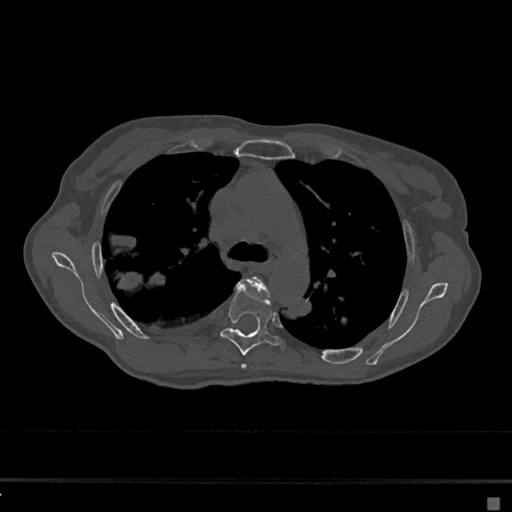
CT including the spine, one axial slice; slice 465 of 797 in the series (ordered by position); reconstruction kernel Br40s/3; 120 kVp; bone window (W 1800 / L 400 HU); 512 × 512 image matrix. Female patient, age 68 years. Case-level facts recorded for this patient, not image findings: primary cancer: renal.
Outlined on this slice (semi-automatic segmentation, software-assisted and operator-edited):
- T4 vertebra: bounding box (x1, y1, x2, y2) in pixels: (241, 276, 270, 369)
- T5 vertebra: (220, 286, 286, 355)